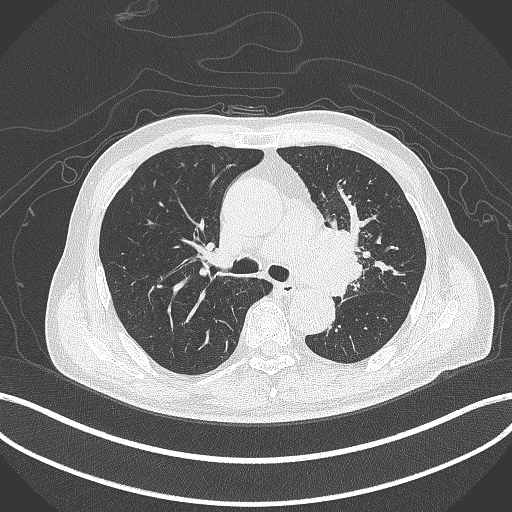
Chest CT, one axial slice. Position 276 of 417 along the scan axis. Reconstruction kernel B70f. Lung window (W 1500 / L -600 HU). 1 mm slice thickness. 512 × 512 image matrix, field of view 400 × 400 mm. Male patient, age 77 years. From the clinical record (not read from this slice): clinical TNM (as recorded): T3 N1 M0.
Structures marked on this image (bounding box drawn by a radiologist):
- lung tumour (recorded histology: adenocarcinoma): box from (x=314, y=222) to (x=366, y=293) px